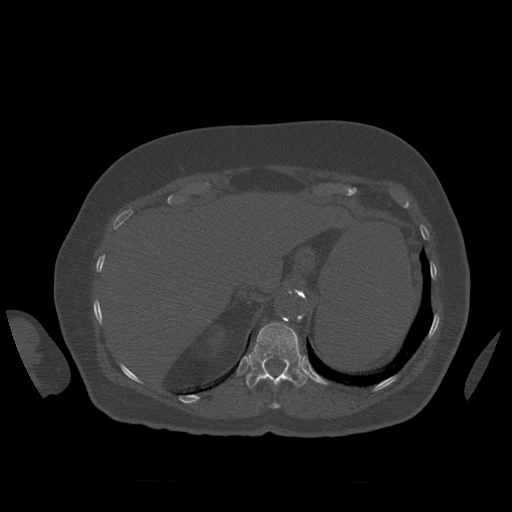
CT including the spine, one axial slice. Slice 305 of 399 in the series (ordered by position). Reconstruction kernel STANDARD. 120 kVp. Bone window (W 1800 / L 400 HU). 1.25 mm slice thickness. 512 × 512 image matrix, field of view 404 × 404 mm. Patient age 81 years. From the clinical record (not read from this slice): primary cancer: renal.
Annotated regions visible in this slice (semi-automatic segmentation, software-assisted and operator-edited):
- T11 vertebra: bounding box (x1, y1, x2, y2) in pixels: (271, 403, 280, 409)
- T12 vertebra: (246, 322, 308, 389)